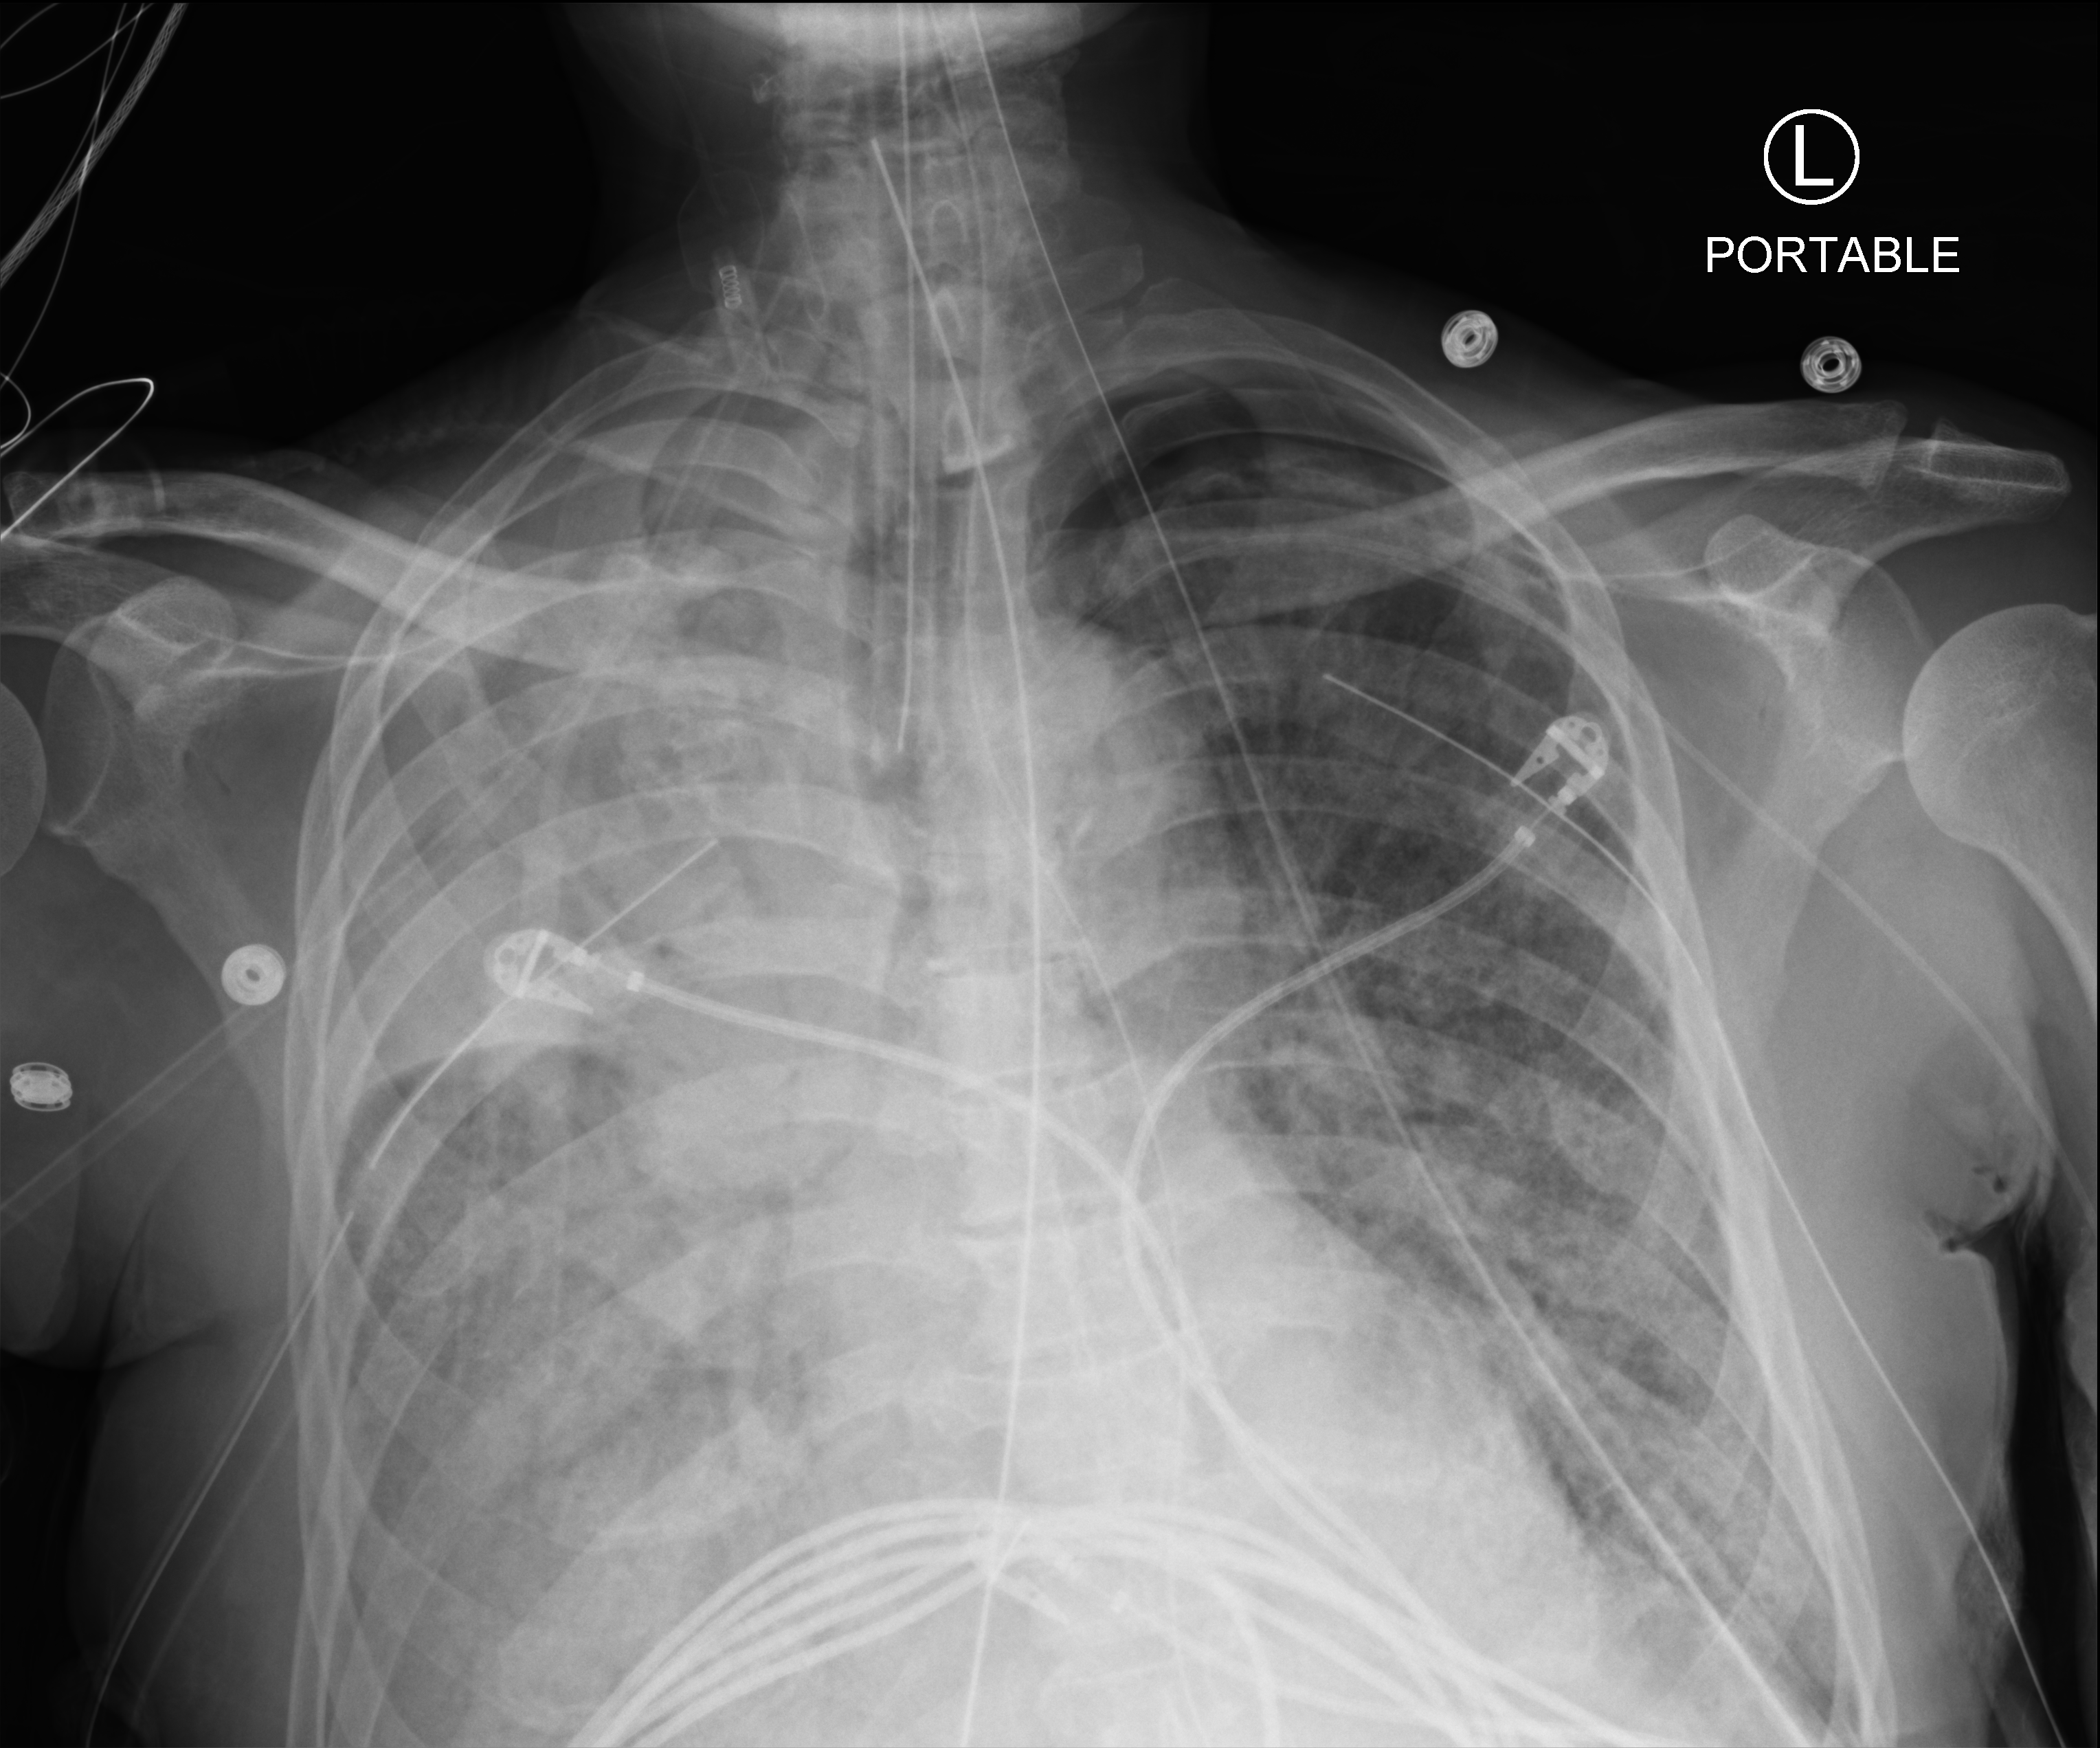
Chest X-ray (portable); anteroposterior (AP) projection. Patient hospitalised with COVID-19; male, aged 60–74 years.
From the hospital-stay record, not from the radiograph (when in the stay this image was taken is not recorded): other chronic lung disease (admission record): no.